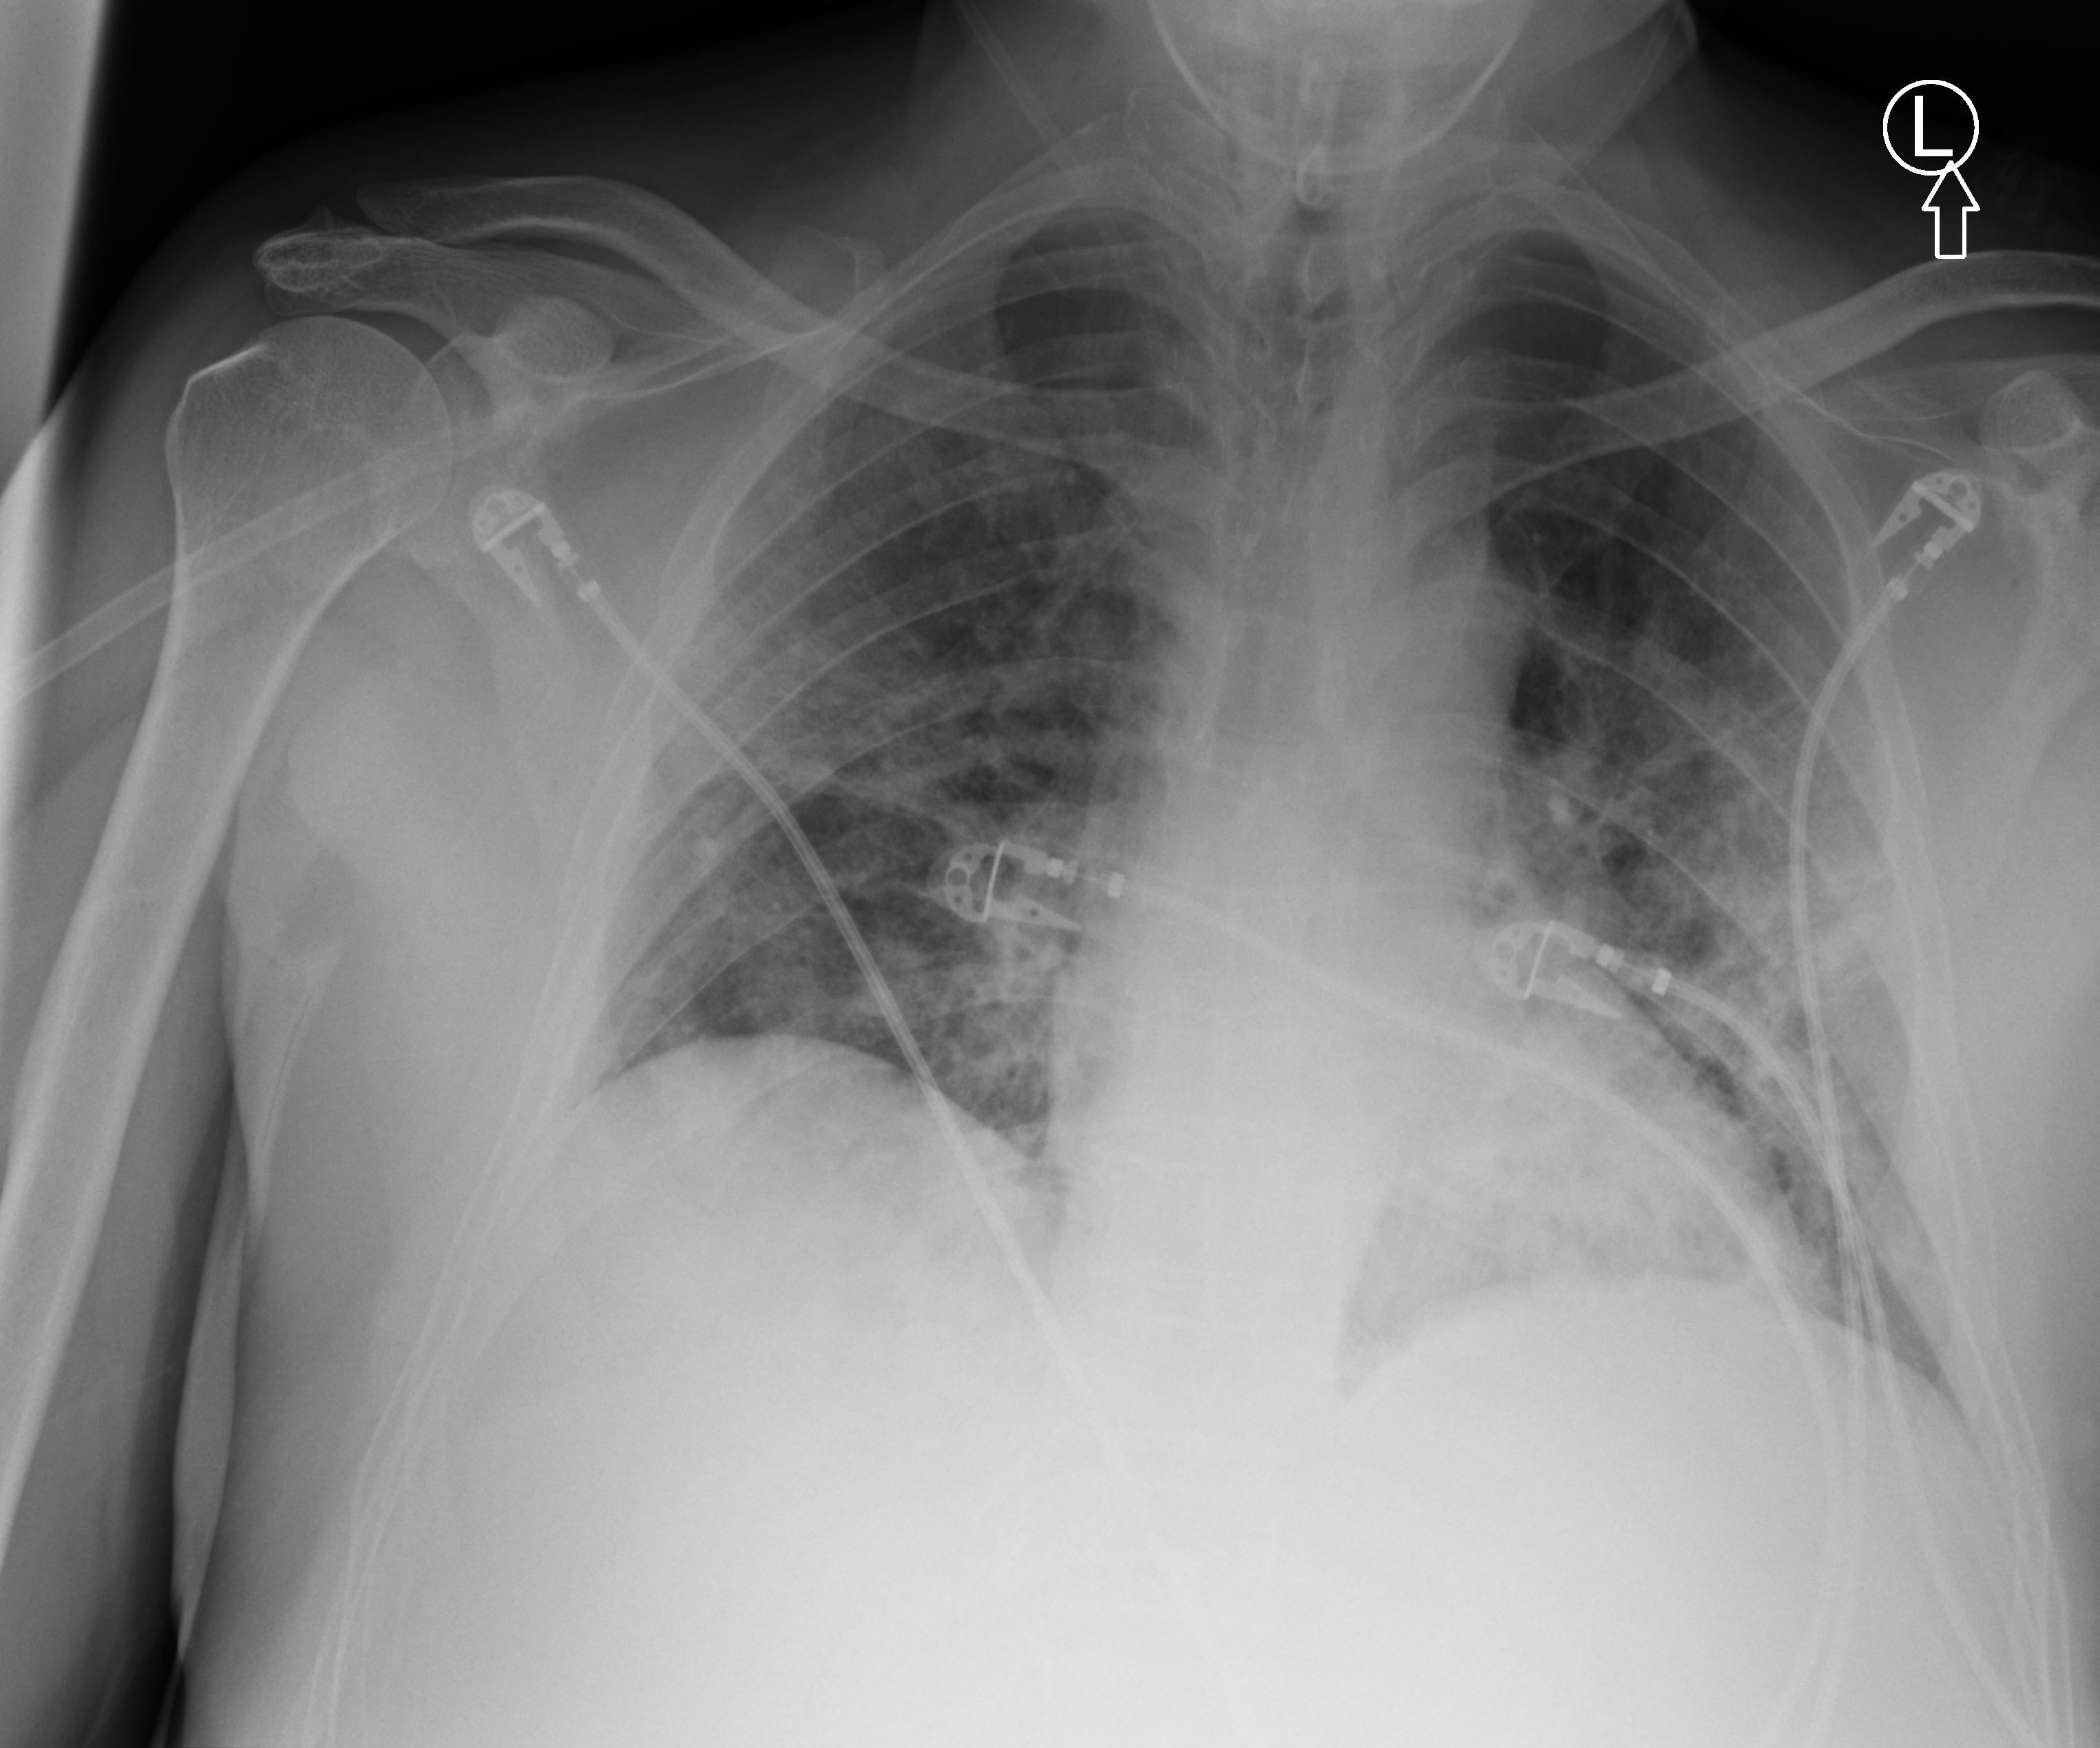
Portable chest radiograph. Male patient hospitalised with COVID-19, age 60–74 years.
Admission-level facts for this patient (not findings on this image; timing relative to this image not recorded): mechanically ventilated during this hospital stay: no.